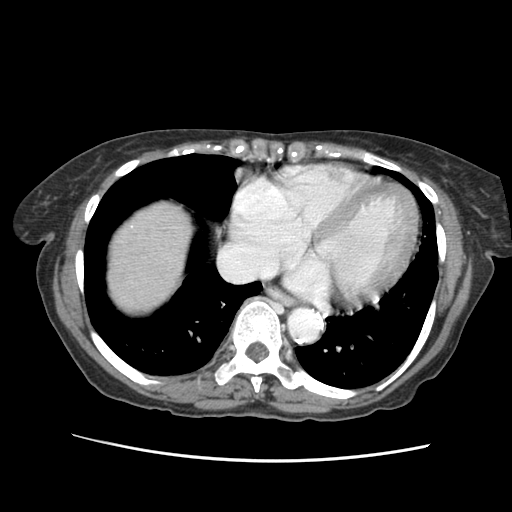
Contrast-enhanced abdominal CT (liver protocol), one axial slice. Slice 57 of 63 in the series (ordered by position). 120 kVp. Soft-tissue window (W 400 / L 40 HU). 2.5 mm slice thickness. 512 × 512 image matrix. From the clinical record (not read from this slice): diagnosis: hepatocellular carcinoma (patient treated with transarterial chemoembolisation; whether this scan precedes or follows treatment is not stated here); TNM stage (as recorded): Stage-I; Child-Pugh class: B; tumour differentiation: well differentiated.
Annotated regions visible in this slice (semi-automatic segmentation, software-assisted and operator-edited):
- liver parenchyma outside the tumour (the mass and vessels are separate outlines, so this box may not span the whole liver): bounding box [x1, y1, x2, y2] px = [112, 206, 184, 302]